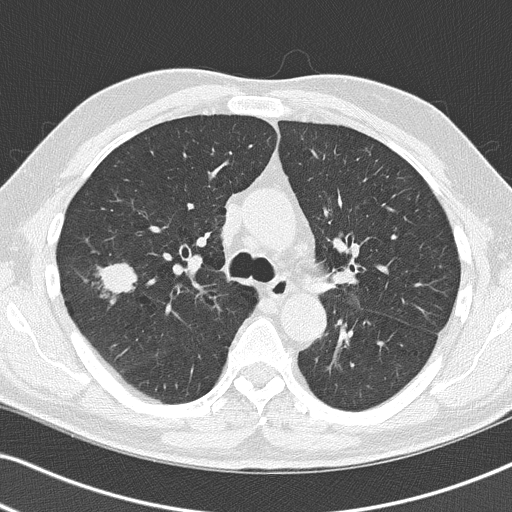
Low-dose screening chest CT, one axial slice. Slice 86 of 140 in the series (ordered by position). Reconstruction kernel B50f. 120 kVp. Lung window (W 1500 / L -600 HU). 512 × 512 image matrix, field of view 330 × 330 mm.
Annotated regions visible in this slice (manually delineated by an expert):
- lesion 1 (tumor, upper lobe of right lung): bounding box [x1, y1, x2, y2] px = [100, 263, 137, 295]